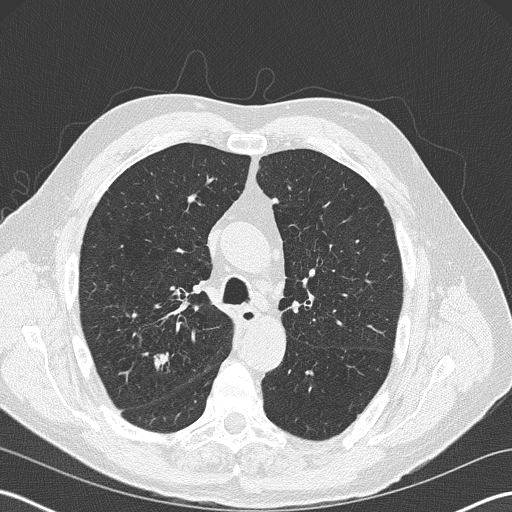
Low-dose screening chest CT, one axial slice; position 130 of 199 along the scan axis; reconstruction kernel B50f; 120 kVp; lung window (W 1500 / L -600 HU); 512 × 512 image matrix, field of view 350 × 350 mm.
Annotated regions visible in this slice (expert manual segmentation):
- lesion 1 (tumor, upper lobe of right lung): bounding box (x1, y1, x2, y2) in pixels: (153, 359, 166, 369)